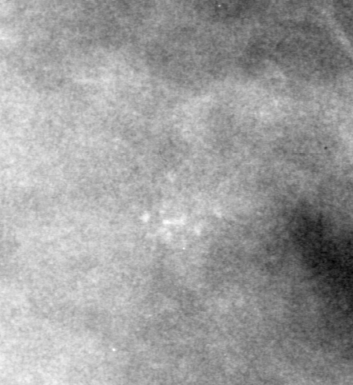
Cropped region of a digitized screen-film mammogram centred on a radiologist-marked abnormality, right breast, CC view, BI-RADS breast density category 4 (scale 1–4).
Calcifications, morphology pleomorphic, distribution clustered; BI-RADS assessment category 4; subtlety rating 4 on a 1 (subtle) to 5 (obvious) scale; pathology result (as recorded, not read from the image): benign.